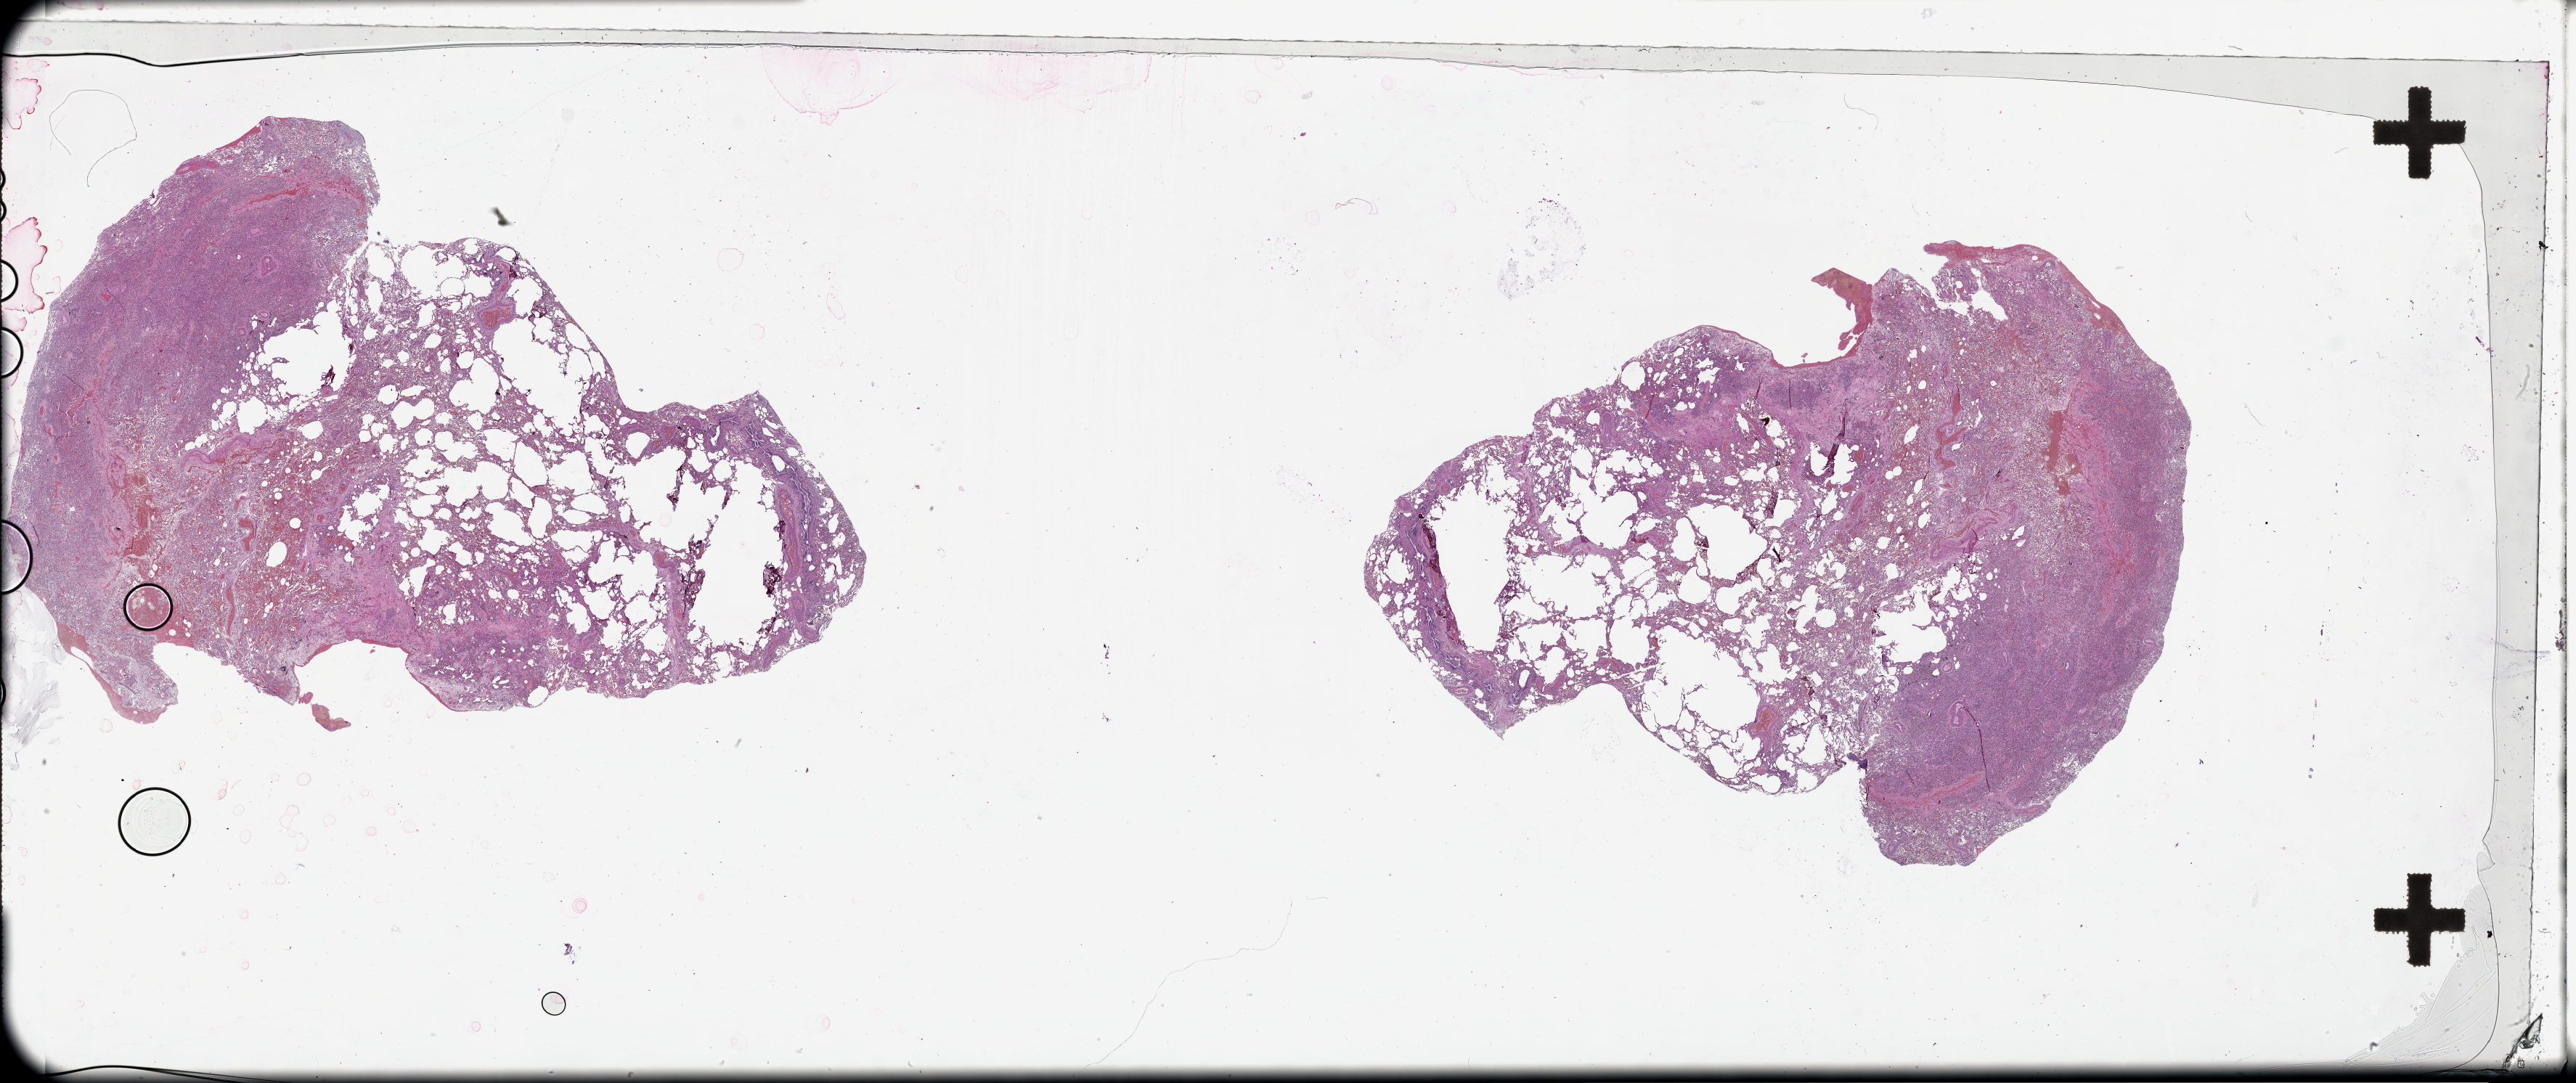
H&E-stained whole-slide image, a low-resolution overview of the entire scanned area, about 57.1 x 24.0 mm (slide scanned at 20x); lung, normal (non-tumour) tissue. Patient: female, age 58 years.
This section: normal (non-tumour) tissue from the same patient. Patient diagnosis (cohort enrolment): squamous cell carcinoma (lung).